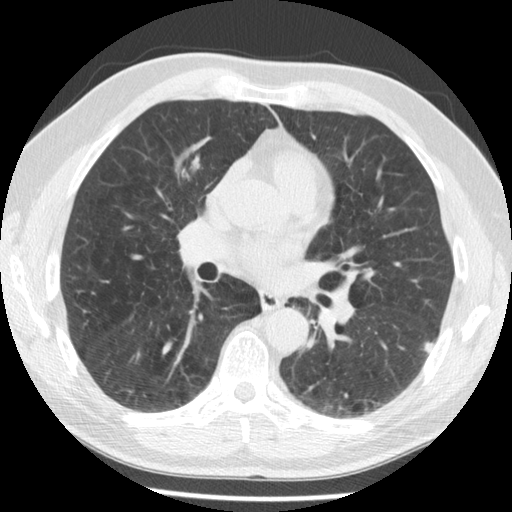
Chest CT (low-dose screening protocol), one axial image; second screening round (one year after baseline); lung window (W 1500 / L -600 HU); 2.5 mm slice thickness. Male participant, aged 57 years at enrolment.
Lesion marked by an expert reader, bounding box (x1, y1, x2, y2) in pixels: (411, 328, 446, 364). The exam's reader record, not a measurement of the box and not confirmed to be the same lesion: non-calcified nodule or mass ≥4 mm, left lower lobe, 6 × 5 mm, poorly defined margins, soft tissue attenuation, pre-existing on the prior screen: yes; interval growth: no. Official screen result: positive, no significant change: stable abnormalities potentially related to lung cancer, unchanged since the prior screening exam. Later outcome: lung cancer diagnosed 427 days after this screen — non-small cell carcinoma, left lower lobe, stage IV (AJCC 6th edition), 13 mm at pathology.